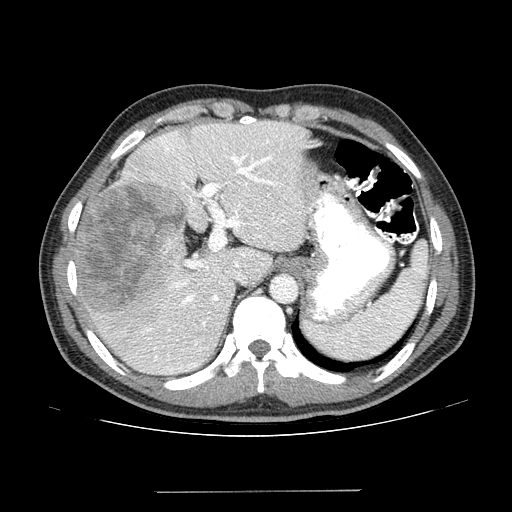
Contrast-enhanced abdominal CT (liver protocol), one axial slice; position 100 of 131 along the scan axis; one of 2 acquisitions stored at this slice position; soft-tissue window (W 400 / L 40 HU); 2.5 mm slice thickness; 512 × 512 image matrix. From the clinical record (not read from this slice): diagnosis: hepatocellular carcinoma (patient treated with transarterial chemoembolisation; whether this scan precedes or follows treatment is not stated here); TNM stage (as recorded): Stage-I; Child-Pugh class: A; tumour nodularity: uninodular.
Outlined on this slice (semi-automatic segmentation, software-assisted and operator-edited):
- liver parenchyma outside the tumour (the mass and vessels are separate outlines, so this box may not span the whole liver): box from (x=74, y=120) to (x=306, y=374) px
- mass: (x=78, y=181)–(x=188, y=315)
- liver vessels: (x=133, y=125)–(x=301, y=372)